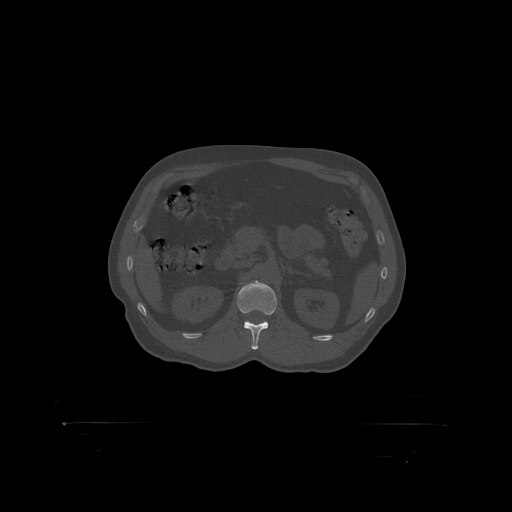
CT including the spine, one axial slice. Slice 320 of 399 in the series (ordered by position). 120 kVp. Bone window (W 1800 / L 400 HU). 1.25 mm slice thickness. 512 × 512 image matrix, field of view 650 × 650 mm. Patient: male, 46 years. Case-level facts recorded for this patient, not image findings: primary cancer: skin.
Annotated regions visible in this slice (semi-automatically segmented with operator editing):
- L1 vertebra: box from (x=237, y=282) to (x=278, y=315) px